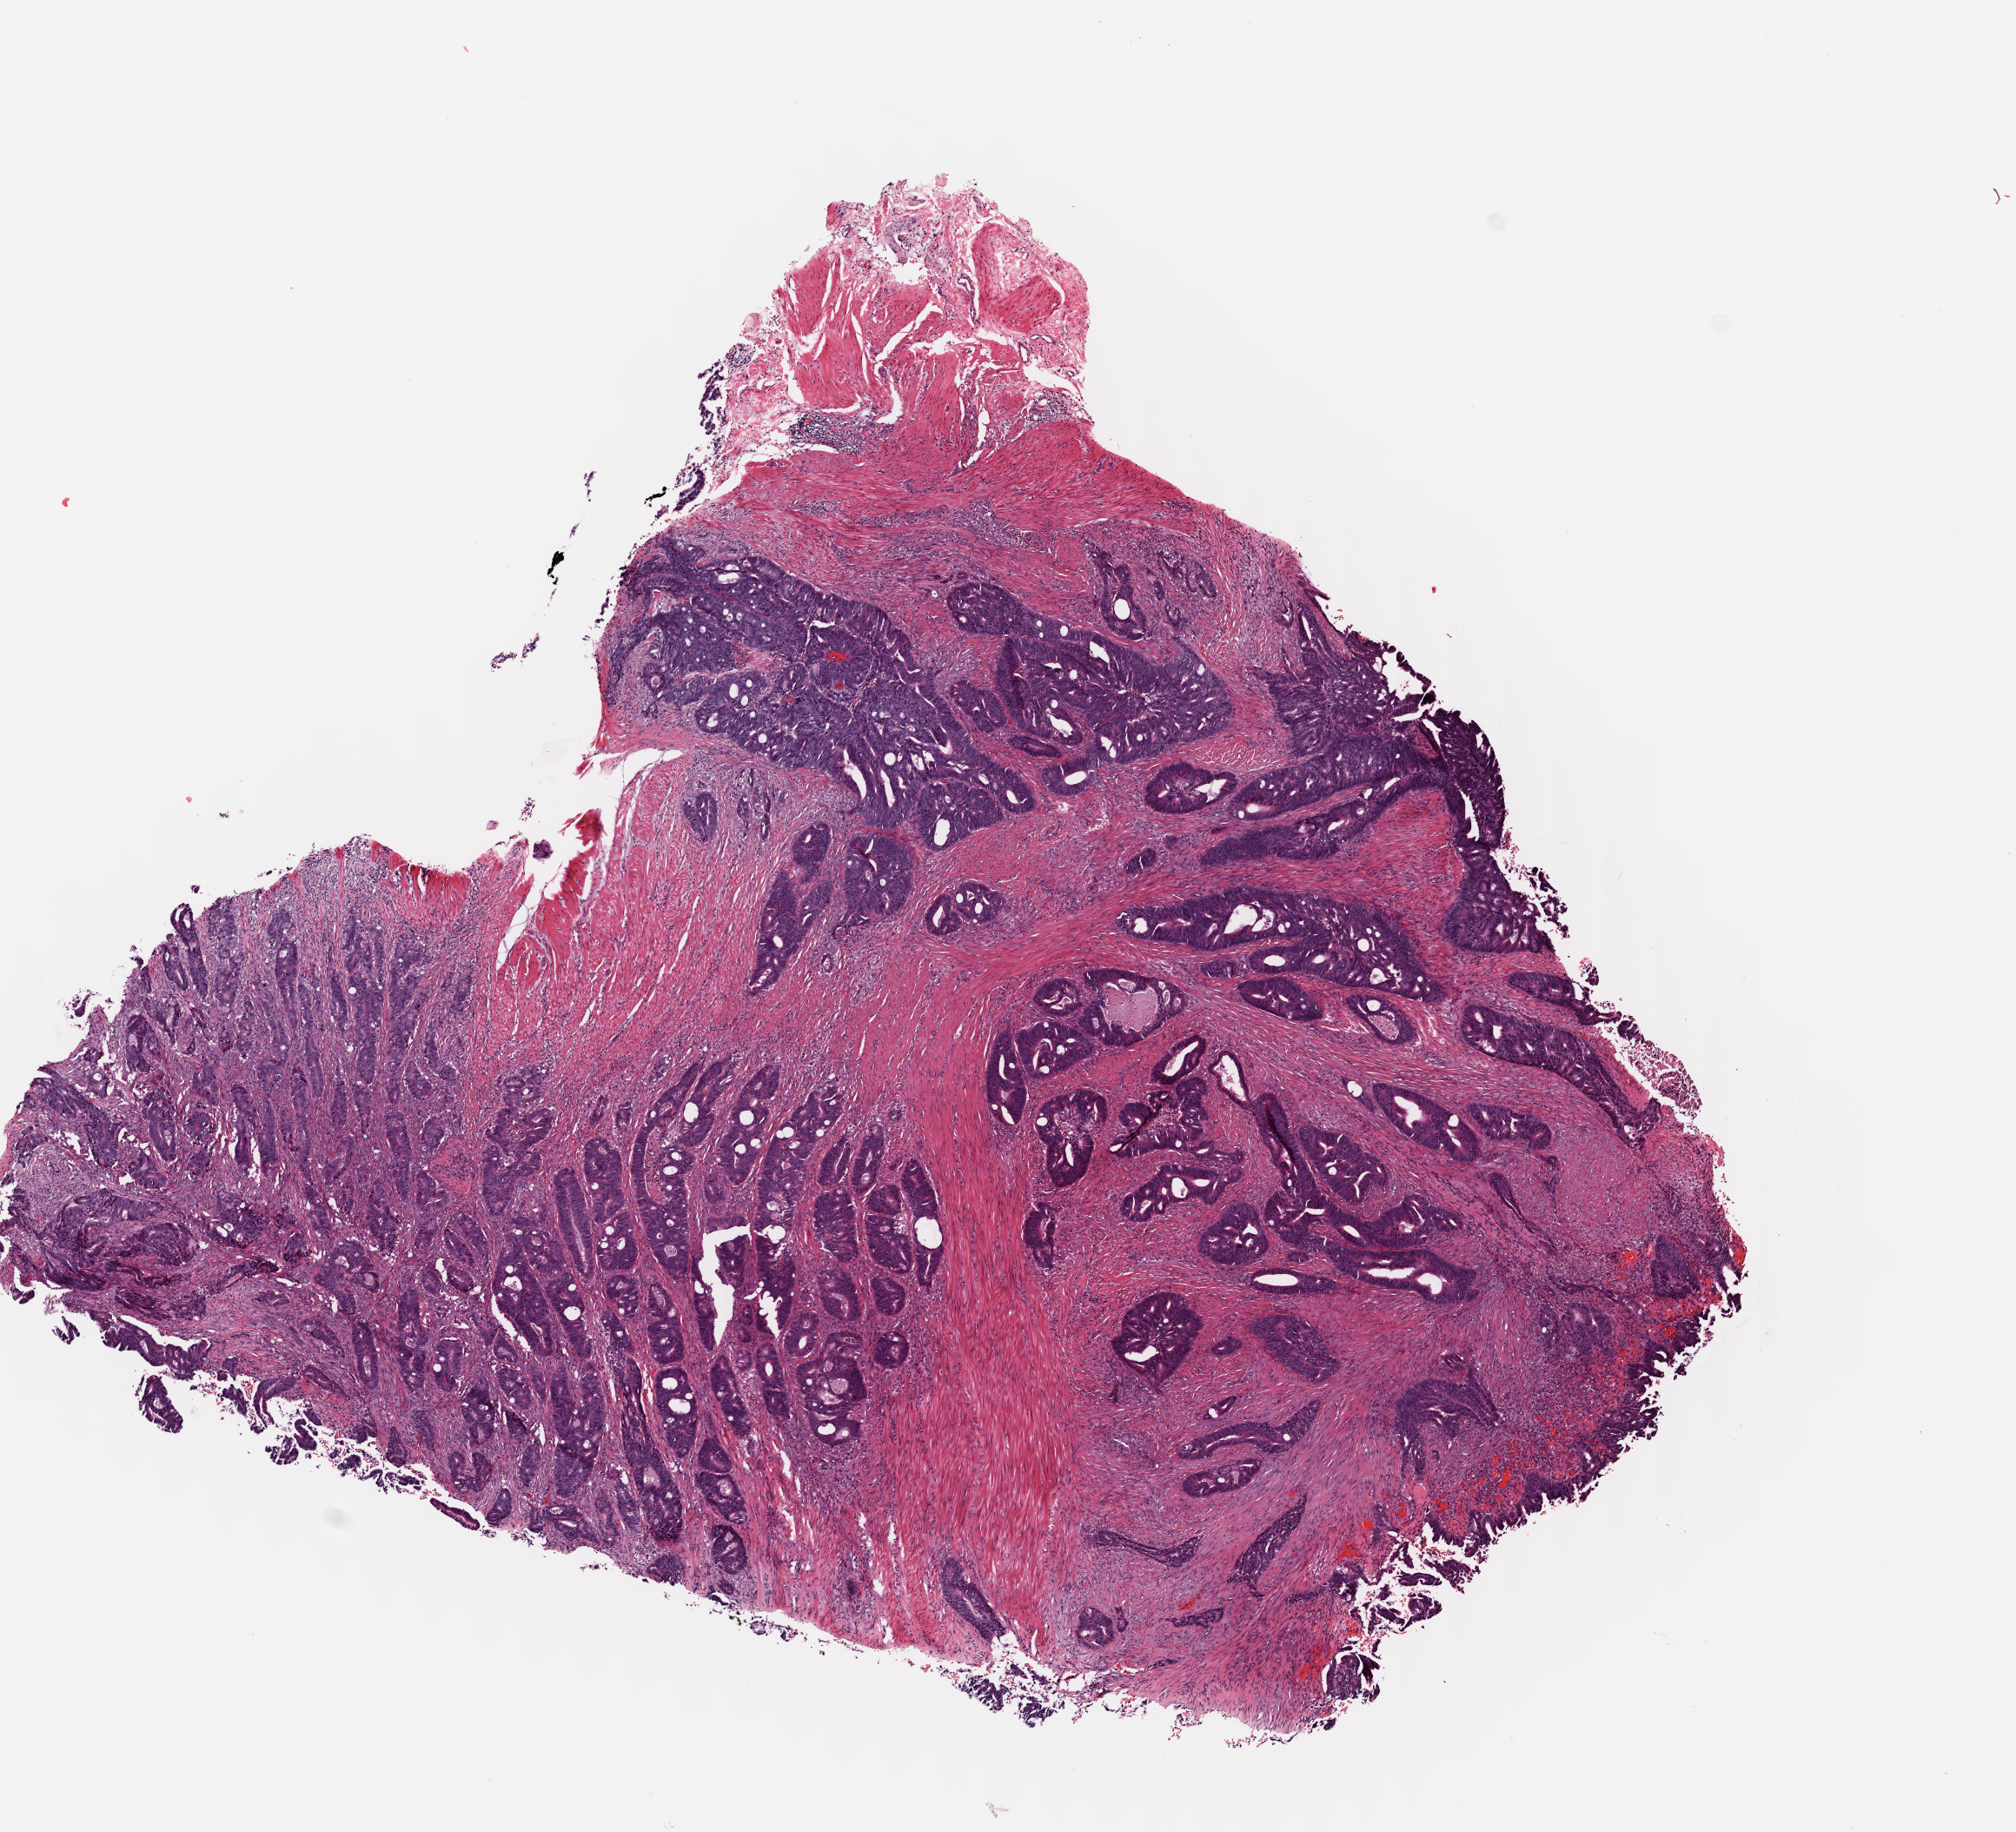
Digitized H&E-stained tissue section (whole slide), low-resolution overview of the scanned area, about 9.1 x 8.3 mm, frozen section from the bottom of the tissue portion, primary tumour sample from the colon. Female patient; age at initial diagnosis 75 years. Composition of this section per pathologist review: tumour cells 85%, tumour nuclei 85%, normal cells 15%, stromal cells 0%, necrosis 0%. Inflammatory infiltration, as recorded: lymphocyte infiltration 0%, monocyte infiltration 0%, neutrophil infiltration 0%.
Pathologic diagnosis: Adenocarcinoma, NOS. Lymph nodes positive (case pathology): 0 of 33 examined. AJCC pathologic stage: I. TNM: T2 N0 M0.